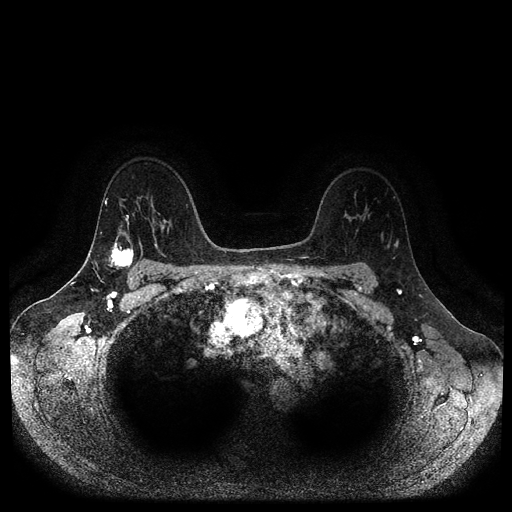
Breast MRI (dynamic contrast-enhanced, multi-phase), one axial slice; slice 73 of 116 in the series (ordered by position); dynamic contrast-enhanced series, time point 2 of 5 at this slice position (early post-contrast); 1.5 T; TE 2.6 ms, TR 5.3 ms; 2 mm slice thickness; 512 × 512 image matrix, field of view 360 × 360 mm. Female patient, age 45 years.
Outlined on this slice (semi-automatically segmented with operator editing):
- breast lesion (labelled 'tumour' in the annotation; benign lesions carry a separate 'benign' label): bounding box (x1, y1, x2, y2) in pixels: (107, 240, 135, 270)